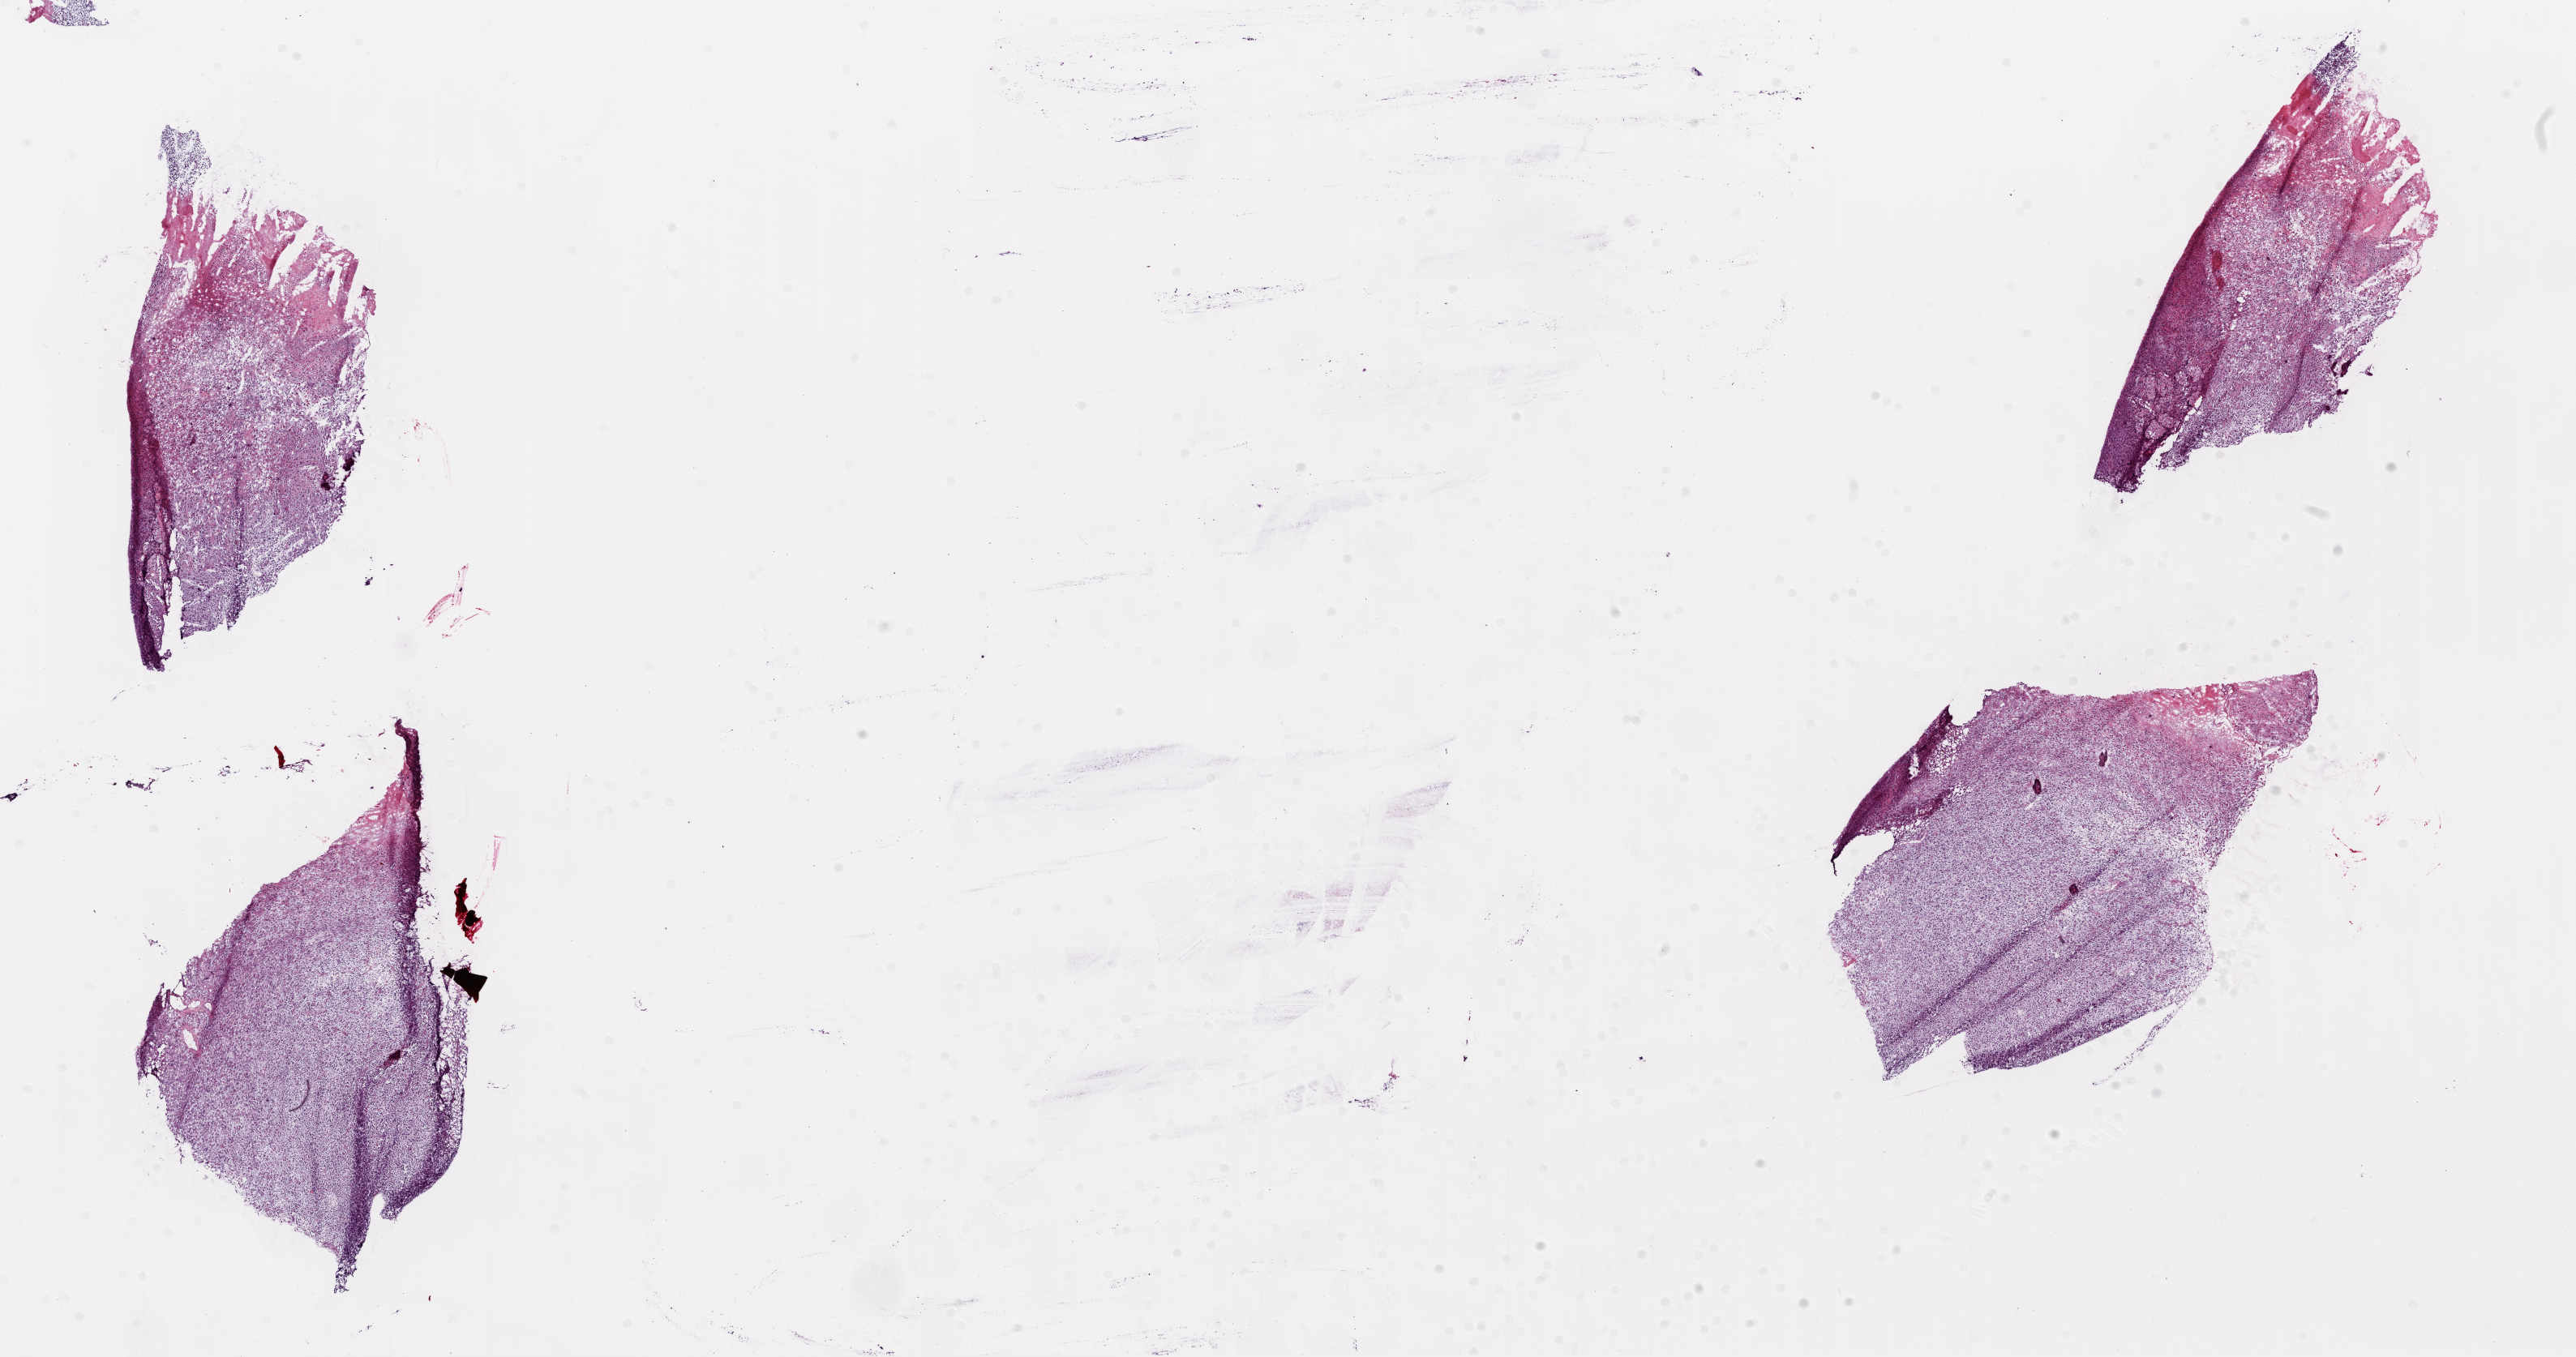
Whole-slide histology image, H&E-stained, shown as a low-resolution overview of the whole scanned area (about 25.6 x 13.5 mm). Frozen section. Primary tumour sample from the brain. Male, age 54 years at initial diagnosis. Pathologist review of this section (percent, as recorded): tumour cells 85%, tumour nuclei 95%, stromal cells 5%, necrosis 10%.
* diagnosis: Glioblastoma